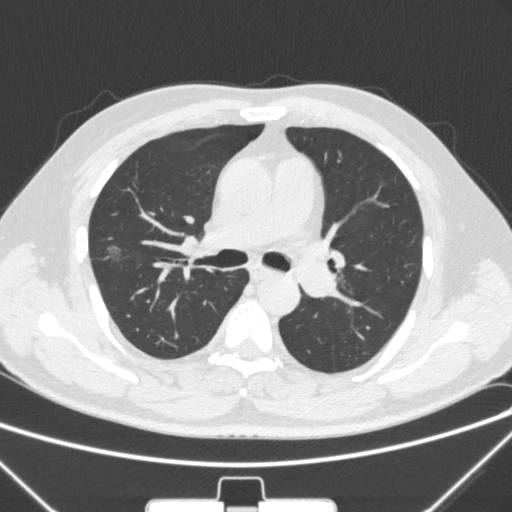
Chest CT, one axial slice. Slice 192 of 320 in the series (ordered by position). 120 kVp. Lung window (W 1500 / L -600 HU). 1 mm slice thickness. 512 × 512 image matrix, field of view 350 × 350 mm. Patient: male, 58 years. Case-level facts recorded for this patient, not image findings: clinical TNM (as recorded): T1c N0 M0; histopathological grade: G2.
Outlined on this slice (bounding box drawn by a radiologist):
- lung tumour (recorded histology: adenocarcinoma): bounding box <102,239,133,271> (left, top, right, bottom; pixels)